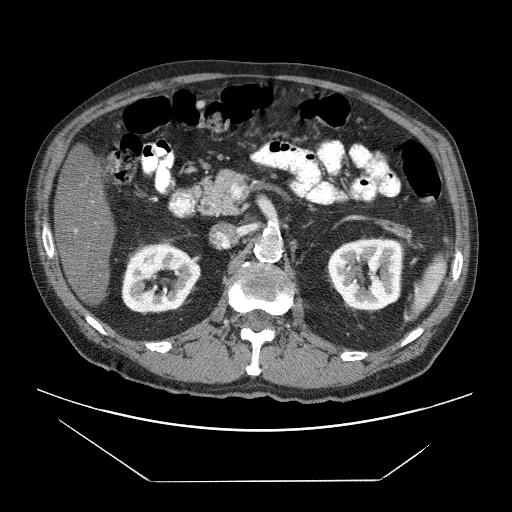
Contrast-enhanced abdominal CT (liver protocol), one axial slice. Slice 20 of 83 in the series (ordered by position). Reconstruction kernel STANDARD. 120 kVp. Soft-tissue window (W 400 / L 40 HU). 2.5 mm slice thickness. 512 × 512 image matrix, field of view 420 × 420 mm. From the clinical record (not read from this slice): diagnosis: hepatocellular carcinoma (patient treated with transarterial chemoembolisation; whether this scan precedes or follows treatment is not stated here); TNM stage (as recorded): Stage-IVB; Child-Pugh class: B; tumour nodularity: uninodular.
Structures marked on this image (semi-automatic segmentation, software-assisted and operator-edited):
- liver parenchyma outside the tumour (the mass and vessels are separate outlines, so this box may not span the whole liver): bounding box (x1, y1, x2, y2) in pixels: (54, 148, 114, 304)
- liver vessels: (74, 229, 77, 232)